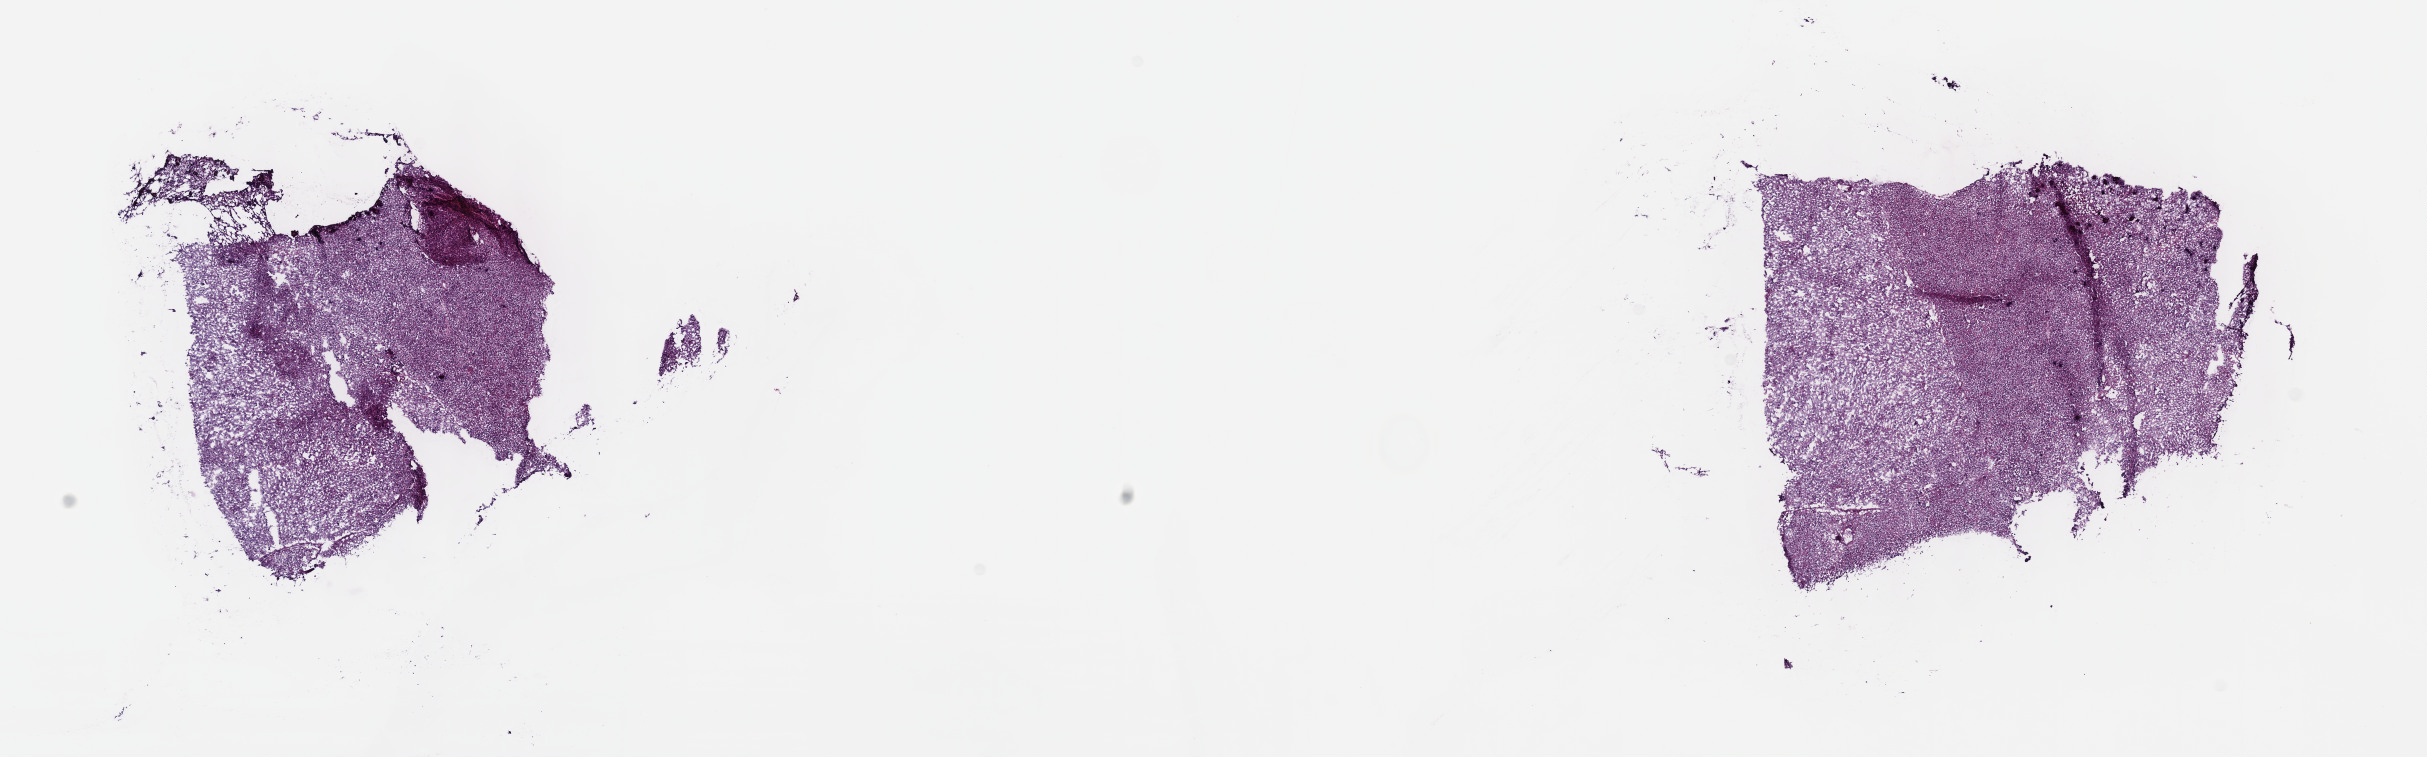
Digitized H&E-stained tissue section (whole slide), low-resolution overview of the scanned area, about 19.6 x 6.1 mm (slide scanned at 40x); frozen section; sample: primary tumour, brain. Male patient; age at initial diagnosis 45 years. Histologic grade: G2 (moderately differentiated). Pathologist review of this section (percent, as recorded): tumour cells 55%, tumour nuclei 90%, normal cells 5%, stromal cells 40%, necrosis 0%. Inflammatory infiltration, as recorded: lymphocyte infiltration 0%, monocyte infiltration 0%, neutrophil infiltration 0%.
* histologic diagnosis: Oligodendroglioma, NOS (cerebrum)
* laterality: left